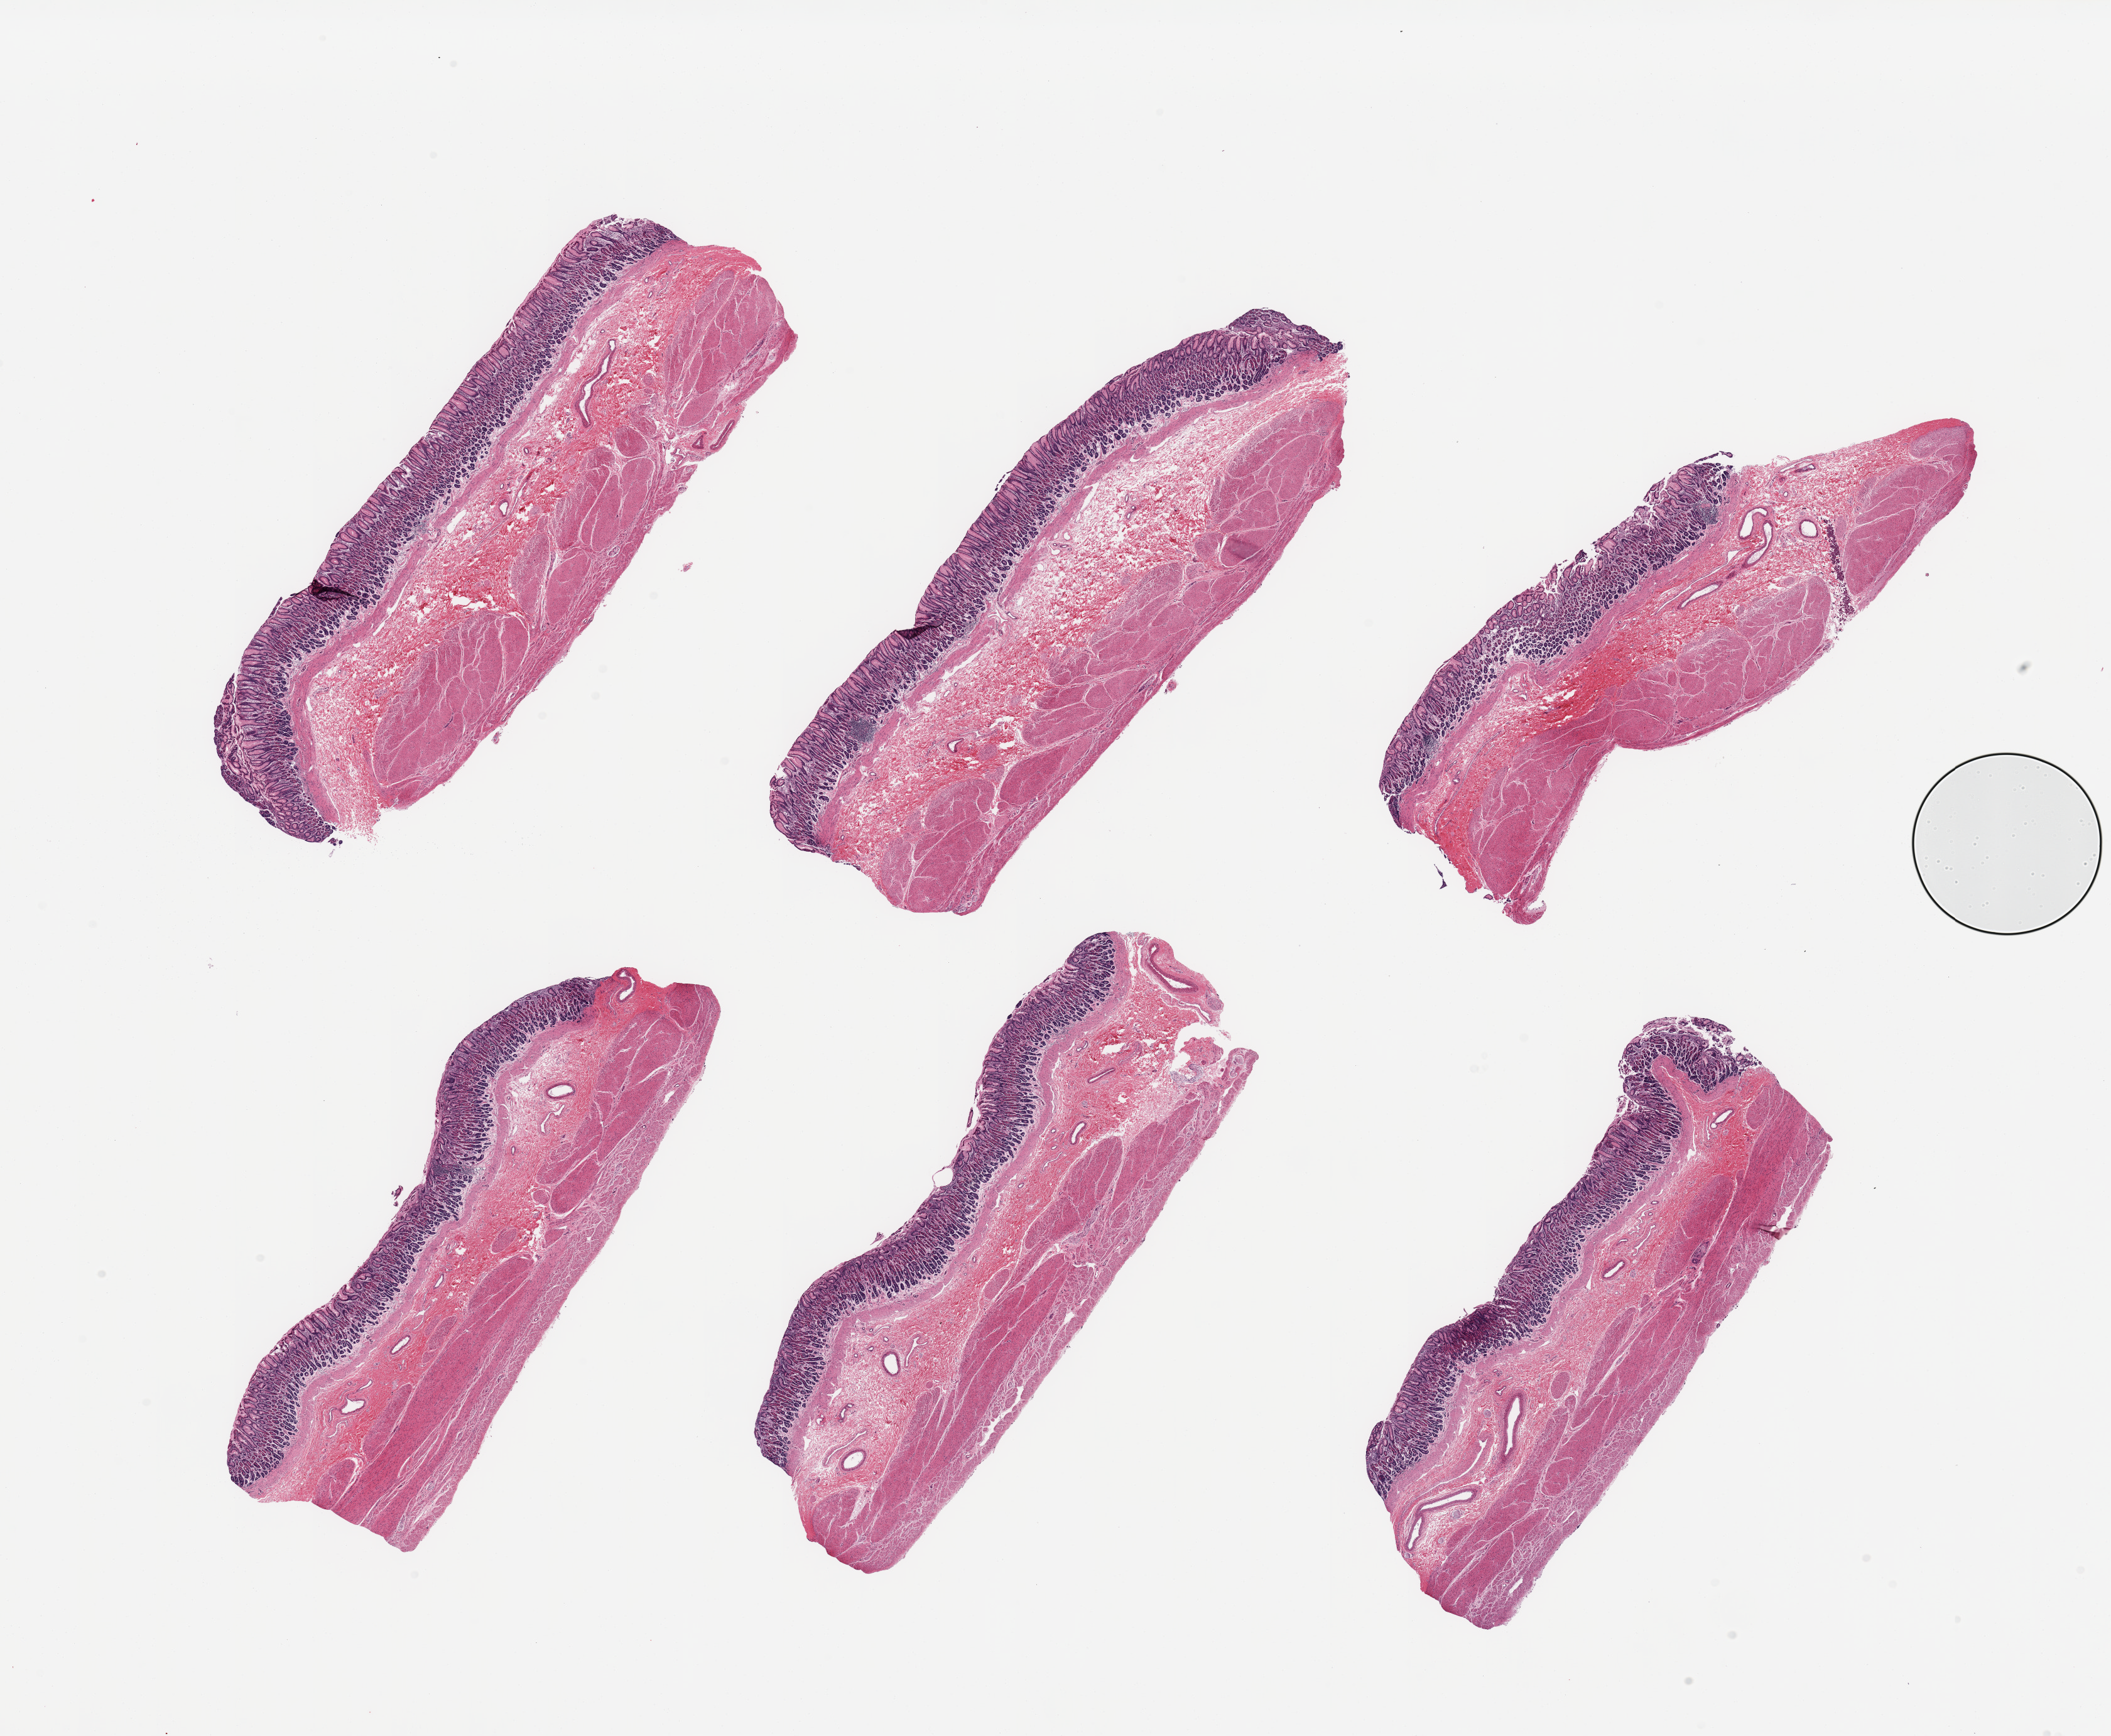
Digitized hematoxylin and eosin (H&E)-stained section, shown as a low-resolution overview of the whole scanned area (about 26.6 x 21.9 mm, from a 20x scan). PAXgene-fixed paraffin-embedded (PFPE) section. Section of stomach (target tissue). Tissue donor sample. Female donor.
* reviewer comment on this tissue sample: 6 pieces; mild to moderately autolyzed gastric mucosa and well preserved muscularis